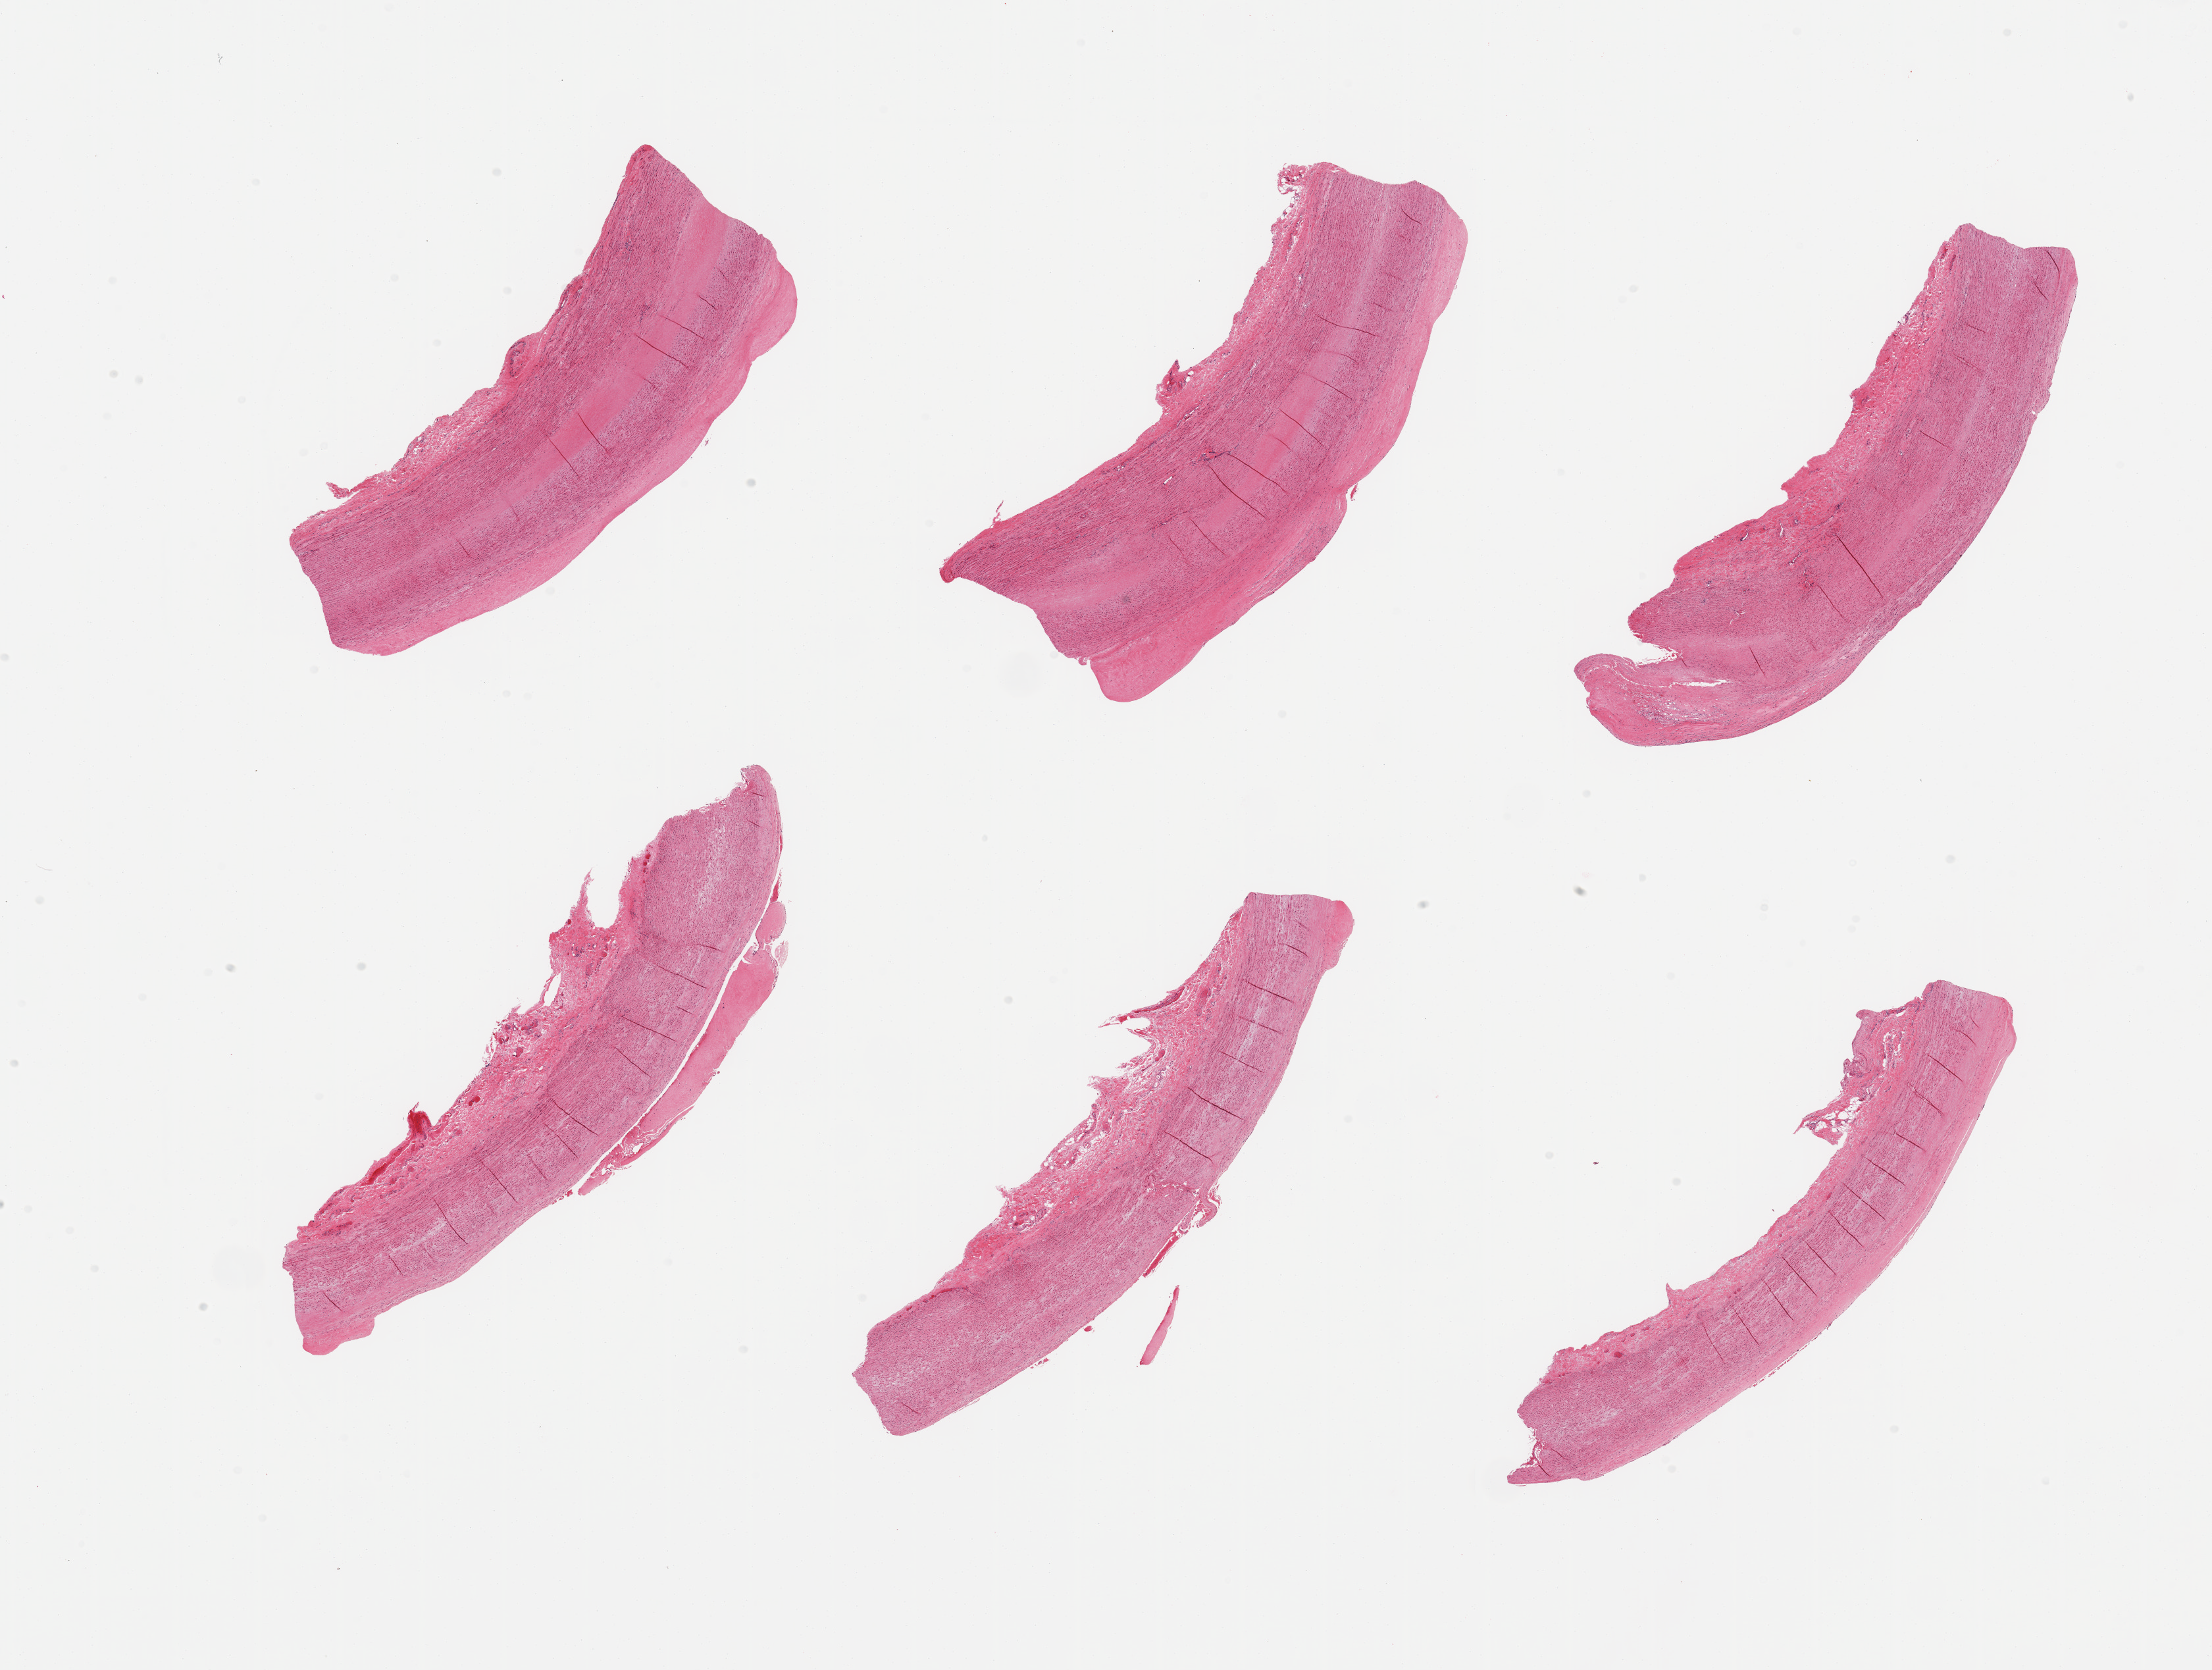
Hematoxylin and eosin (H&E) whole-slide image, brightfield — a low-resolution overview of the entire scanned area, about 26.6 x 20.1 mm (from a 20x scan). PAXgene-fixed paraffin-embedded (PFPE) section. Section of aorta (target tissue). Tissue donor sample.
Review note (as recorded): 6 pieces atherosis up to ~1.5mm thick.